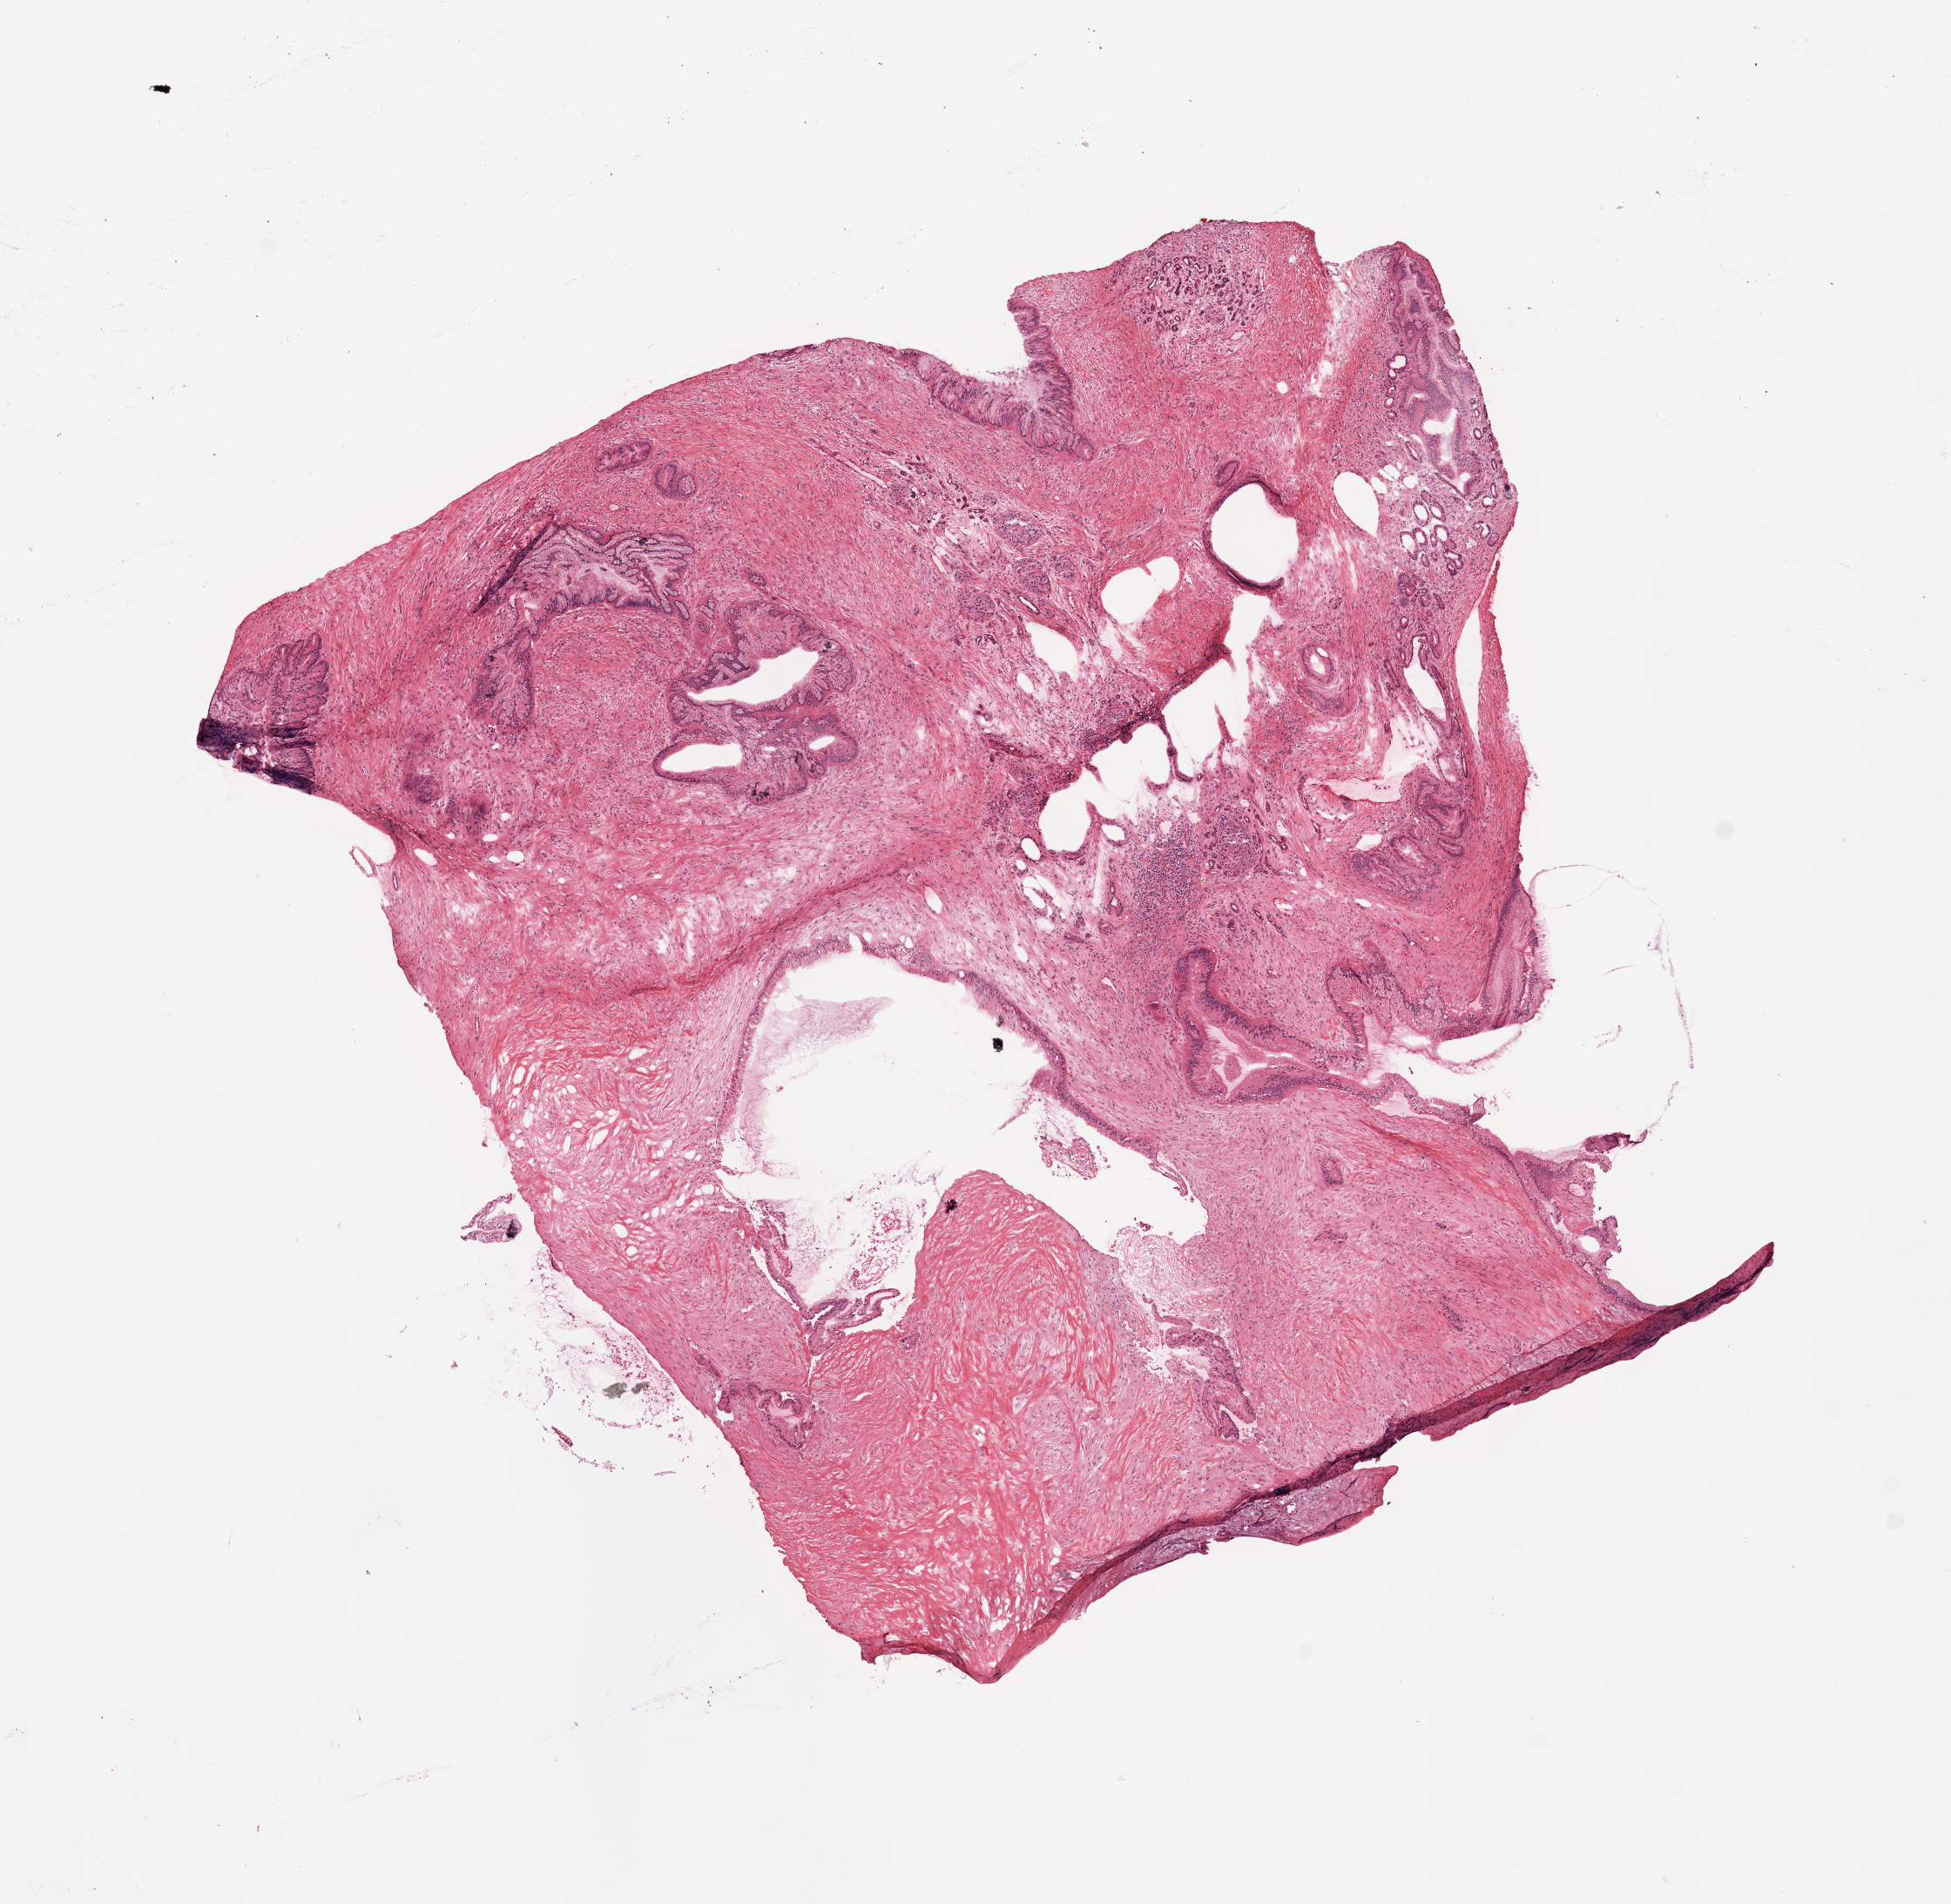
Digitized Hematoxylin and eosin (H&E) stained tissue section (whole slide) — a low-resolution overview of the entire scanned area, about 8.9 x 8.6 mm (slide scanned at 20x); tumour tissue sample, pancreas. Male, 75 y/o.
- patient diagnosis (cohort enrolment): ductal adenocarcinoma (pancreas)